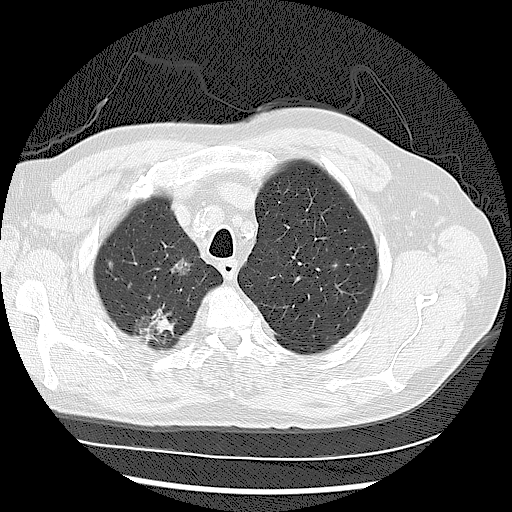
Low-dose screening chest CT, one axial slice; reconstruction kernel LUNG; 120 kVp; lung window (W 1500 / L -600 HU); 512 × 512 image matrix.
Structures marked on this image (outlined manually by an expert reader):
- lesion 1 (tumor, upper lobe of right lung): bounding box <140,310,174,343> (left, top, right, bottom; pixels)